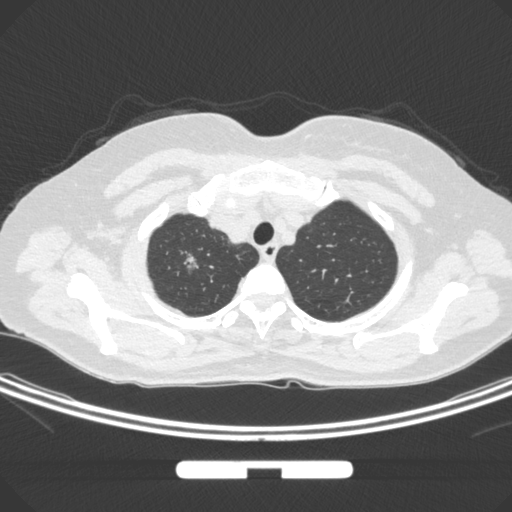
Chest CT, one axial slice. Slice 255 of 295 in the series (ordered by position). 120 kVp. Lung window (W 1500 / L -600 HU). 1 mm slice thickness. 512 × 512 image matrix. Patient: female, 58 years. From the clinical record (not read from this slice): clinical TNM (as recorded): T1b N0 M0.
Annotated regions visible in this slice (bounding box drawn by a radiologist):
- lung tumour (recorded histology: adenocarcinoma): bounding box [x1, y1, x2, y2] px = [181, 250, 209, 283]